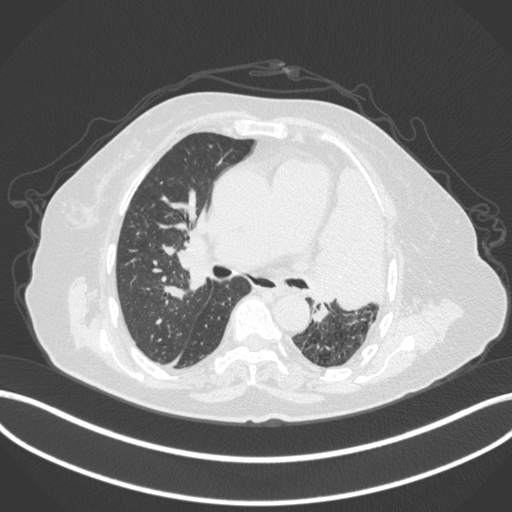
Chest CT, one axial slice; slice 223 of 399 in the series (ordered by position); reconstruction kernel B31f; 120 kVp; lung window (W 1500 / L -600 HU); 512 × 512 image matrix, field of view 400 × 400 mm. Female patient, age 75 years. Case-level facts recorded for this patient, not image findings: clinical TNM (as recorded): T3 N3 M1.
Structures marked on this image (rectangle marked by the reading radiologist):
- lung tumour (recorded histology: adenocarcinoma): bounding box (x1, y1, x2, y2) in pixels: (297, 155, 390, 311)